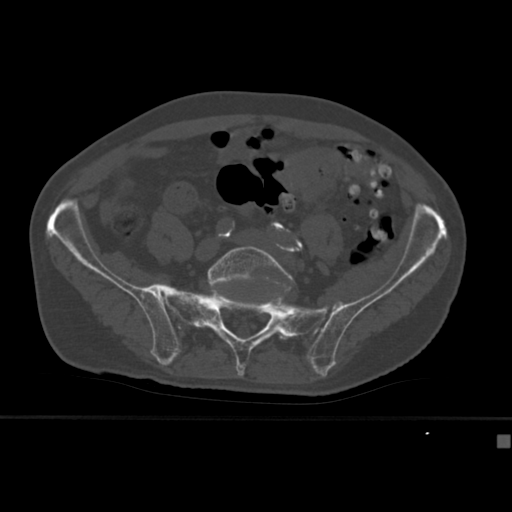
CT including the spine, one axial slice. Position 76 of 430 along the scan axis. Reconstruction kernel Br40s. 120 kVp. Bone window (W 1800 / L 400 HU). 1.5 mm slice thickness. 512 × 512 image matrix, field of view 337 × 337 mm. Male patient, age 64 years. From the clinical record (not read from this slice): primary cancer: uterus; vertebrae with lytic lesions (as recorded): T1, T4, T5, T7, L5.
Structures marked on this image (semi-automatic segmentation, software-assisted and operator-edited):
- L5 vertebra: bounding box <207,245,294,327> (left, top, right, bottom; pixels)